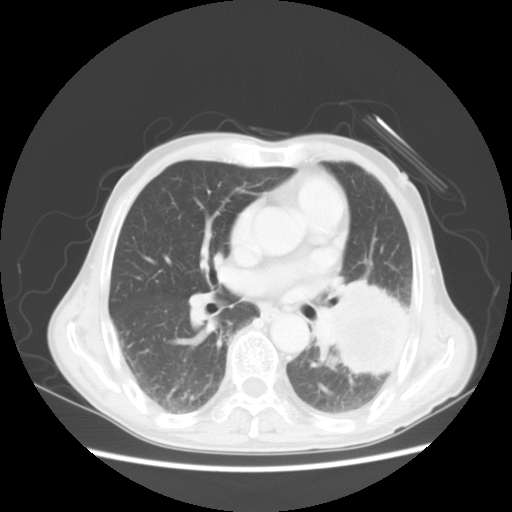
Chest CT, one axial slice; slice 26 of 51 in the series (ordered by position); reconstruction kernel STANDARD; lung window (W 1500 / L -600 HU); 512 × 512 image matrix. Patient: male, 64 years. From the clinical record (not read from this slice): clinical TNM (as recorded): T4 N0 M0; histopathological grade: G2-3.
Structures marked on this image (bounding box drawn by a radiologist):
- lung tumour (recorded histology: squamous cell carcinoma): bounding box [x1, y1, x2, y2] px = [323, 276, 421, 398]